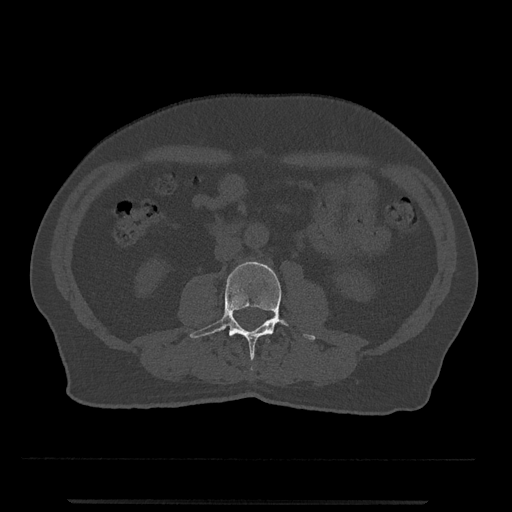
CT including the spine, one axial slice. Slice 202 of 797 in the series (ordered by position). Reconstruction kernel Br40s/3. Bone window (W 1800 / L 400 HU). 0.5 mm slice thickness. 512 × 512 image matrix, field of view 419 × 419 mm. Patient: male, 63 years. Case-level facts recorded for this patient, not image findings: primary cancer: prostate.
Outlined on this slice (semi-automatic segmentation, software-assisted and operator-edited):
- L2 vertebra: bounding box [x1, y1, x2, y2] px = [266, 338, 270, 343]
- L3 vertebra: [189, 261, 316, 360]